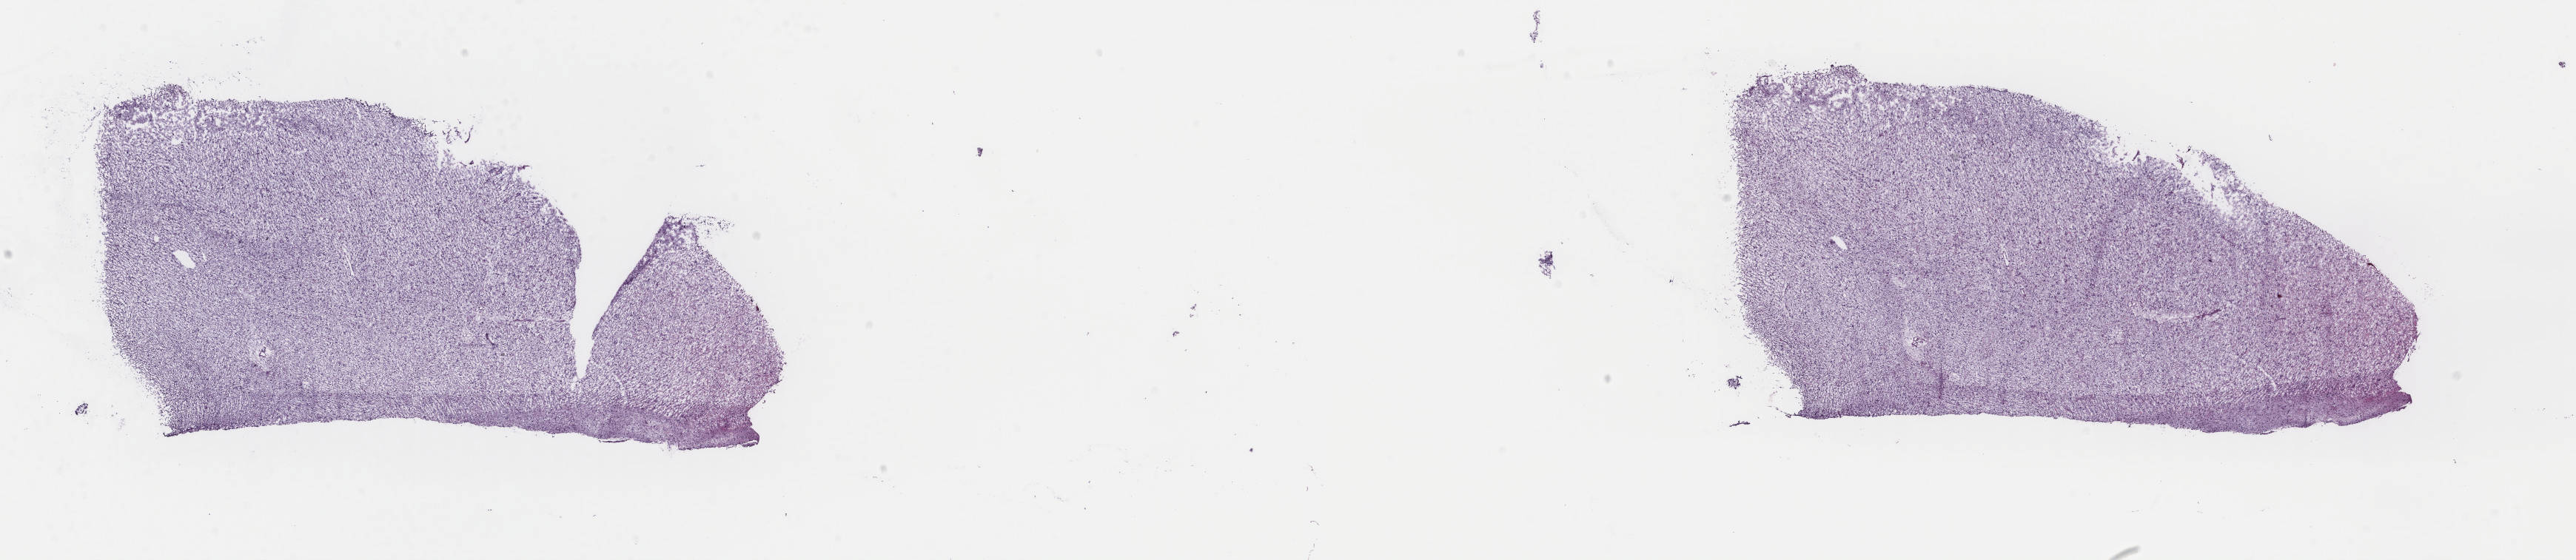
H&E whole-slide image — shown as a low-resolution overview of the whole scanned area (about 27.6 x 6.0 mm). Frozen section. Brain, primary tumour sample. Female patient; age at initial diagnosis 27 years.
Histologic diagnosis: Mixed glioma (temporal lobe).